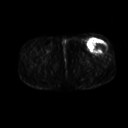
FDG PET of an extremity soft-tissue mass (from a PET/CT study), one axial slice. Slice 243 of 267 in the series (ordered by position). 128 × 128 image matrix, field of view 500 × 500 mm. Patient: male, 64 years. Case-level facts recorded for this patient, not image findings: histological type: extraskeletal osteosarcoma; grade: high; site of the primary tumour: thigh.
Outlined on this slice (expert contour drawn on MRI and transferred to this co-registered scan by the dataset authors):
- gross tumour volume (mass): bounding box (x1, y1, x2, y2) in pixels: (87, 40, 107, 53)